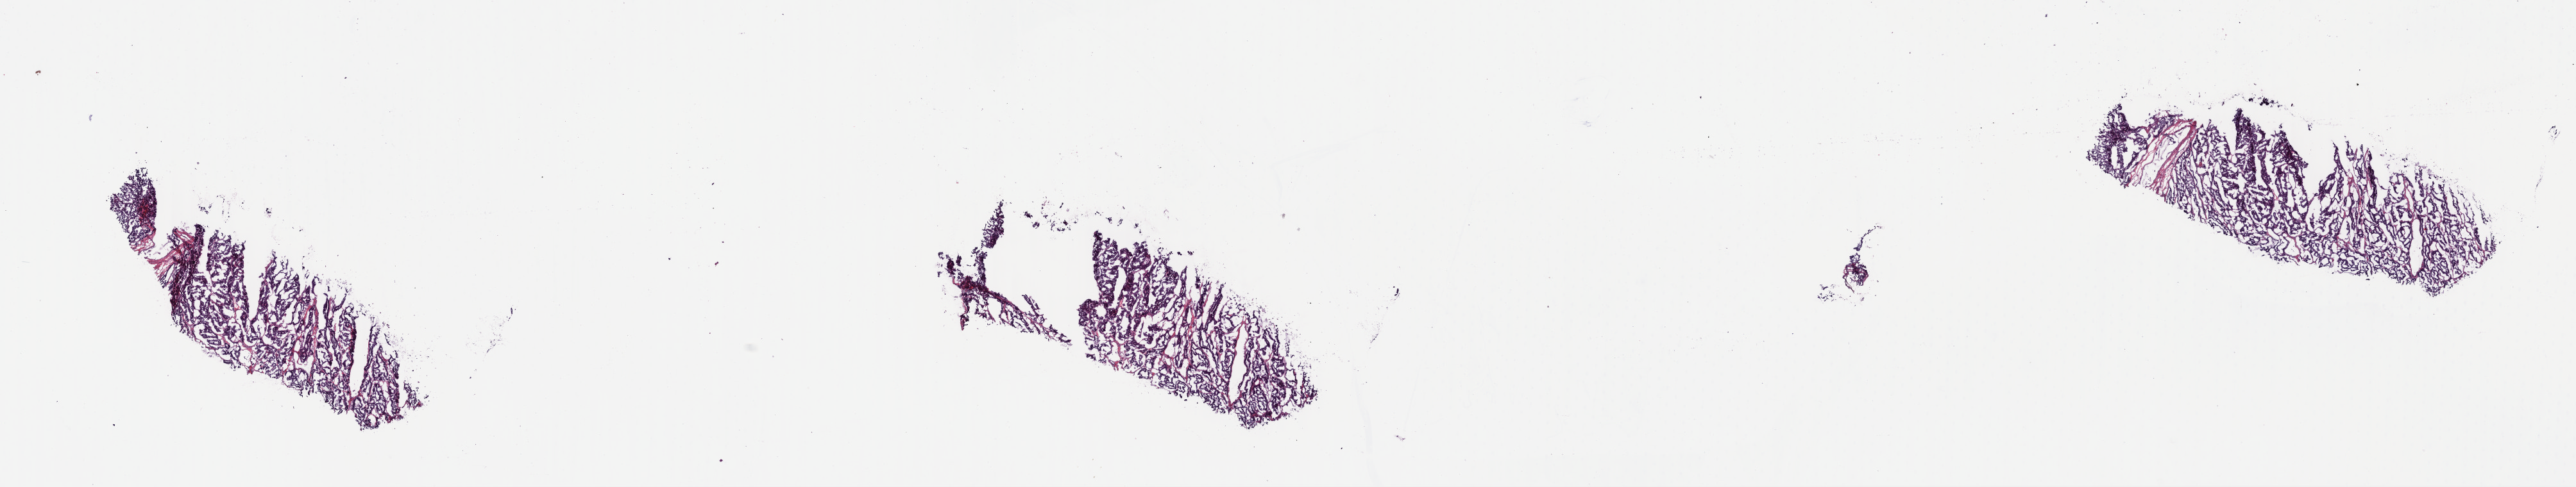
Digitized H&E tissue section (whole slide) — shown as a low-resolution overview of the whole scanned area (about 31.6 x 6.0 mm); frozen section; thyroid, primary tumour sample. Male, age 63 years at initial diagnosis.
Diagnosis: Papillary adenocarcinoma, NOS (thyroid gland).